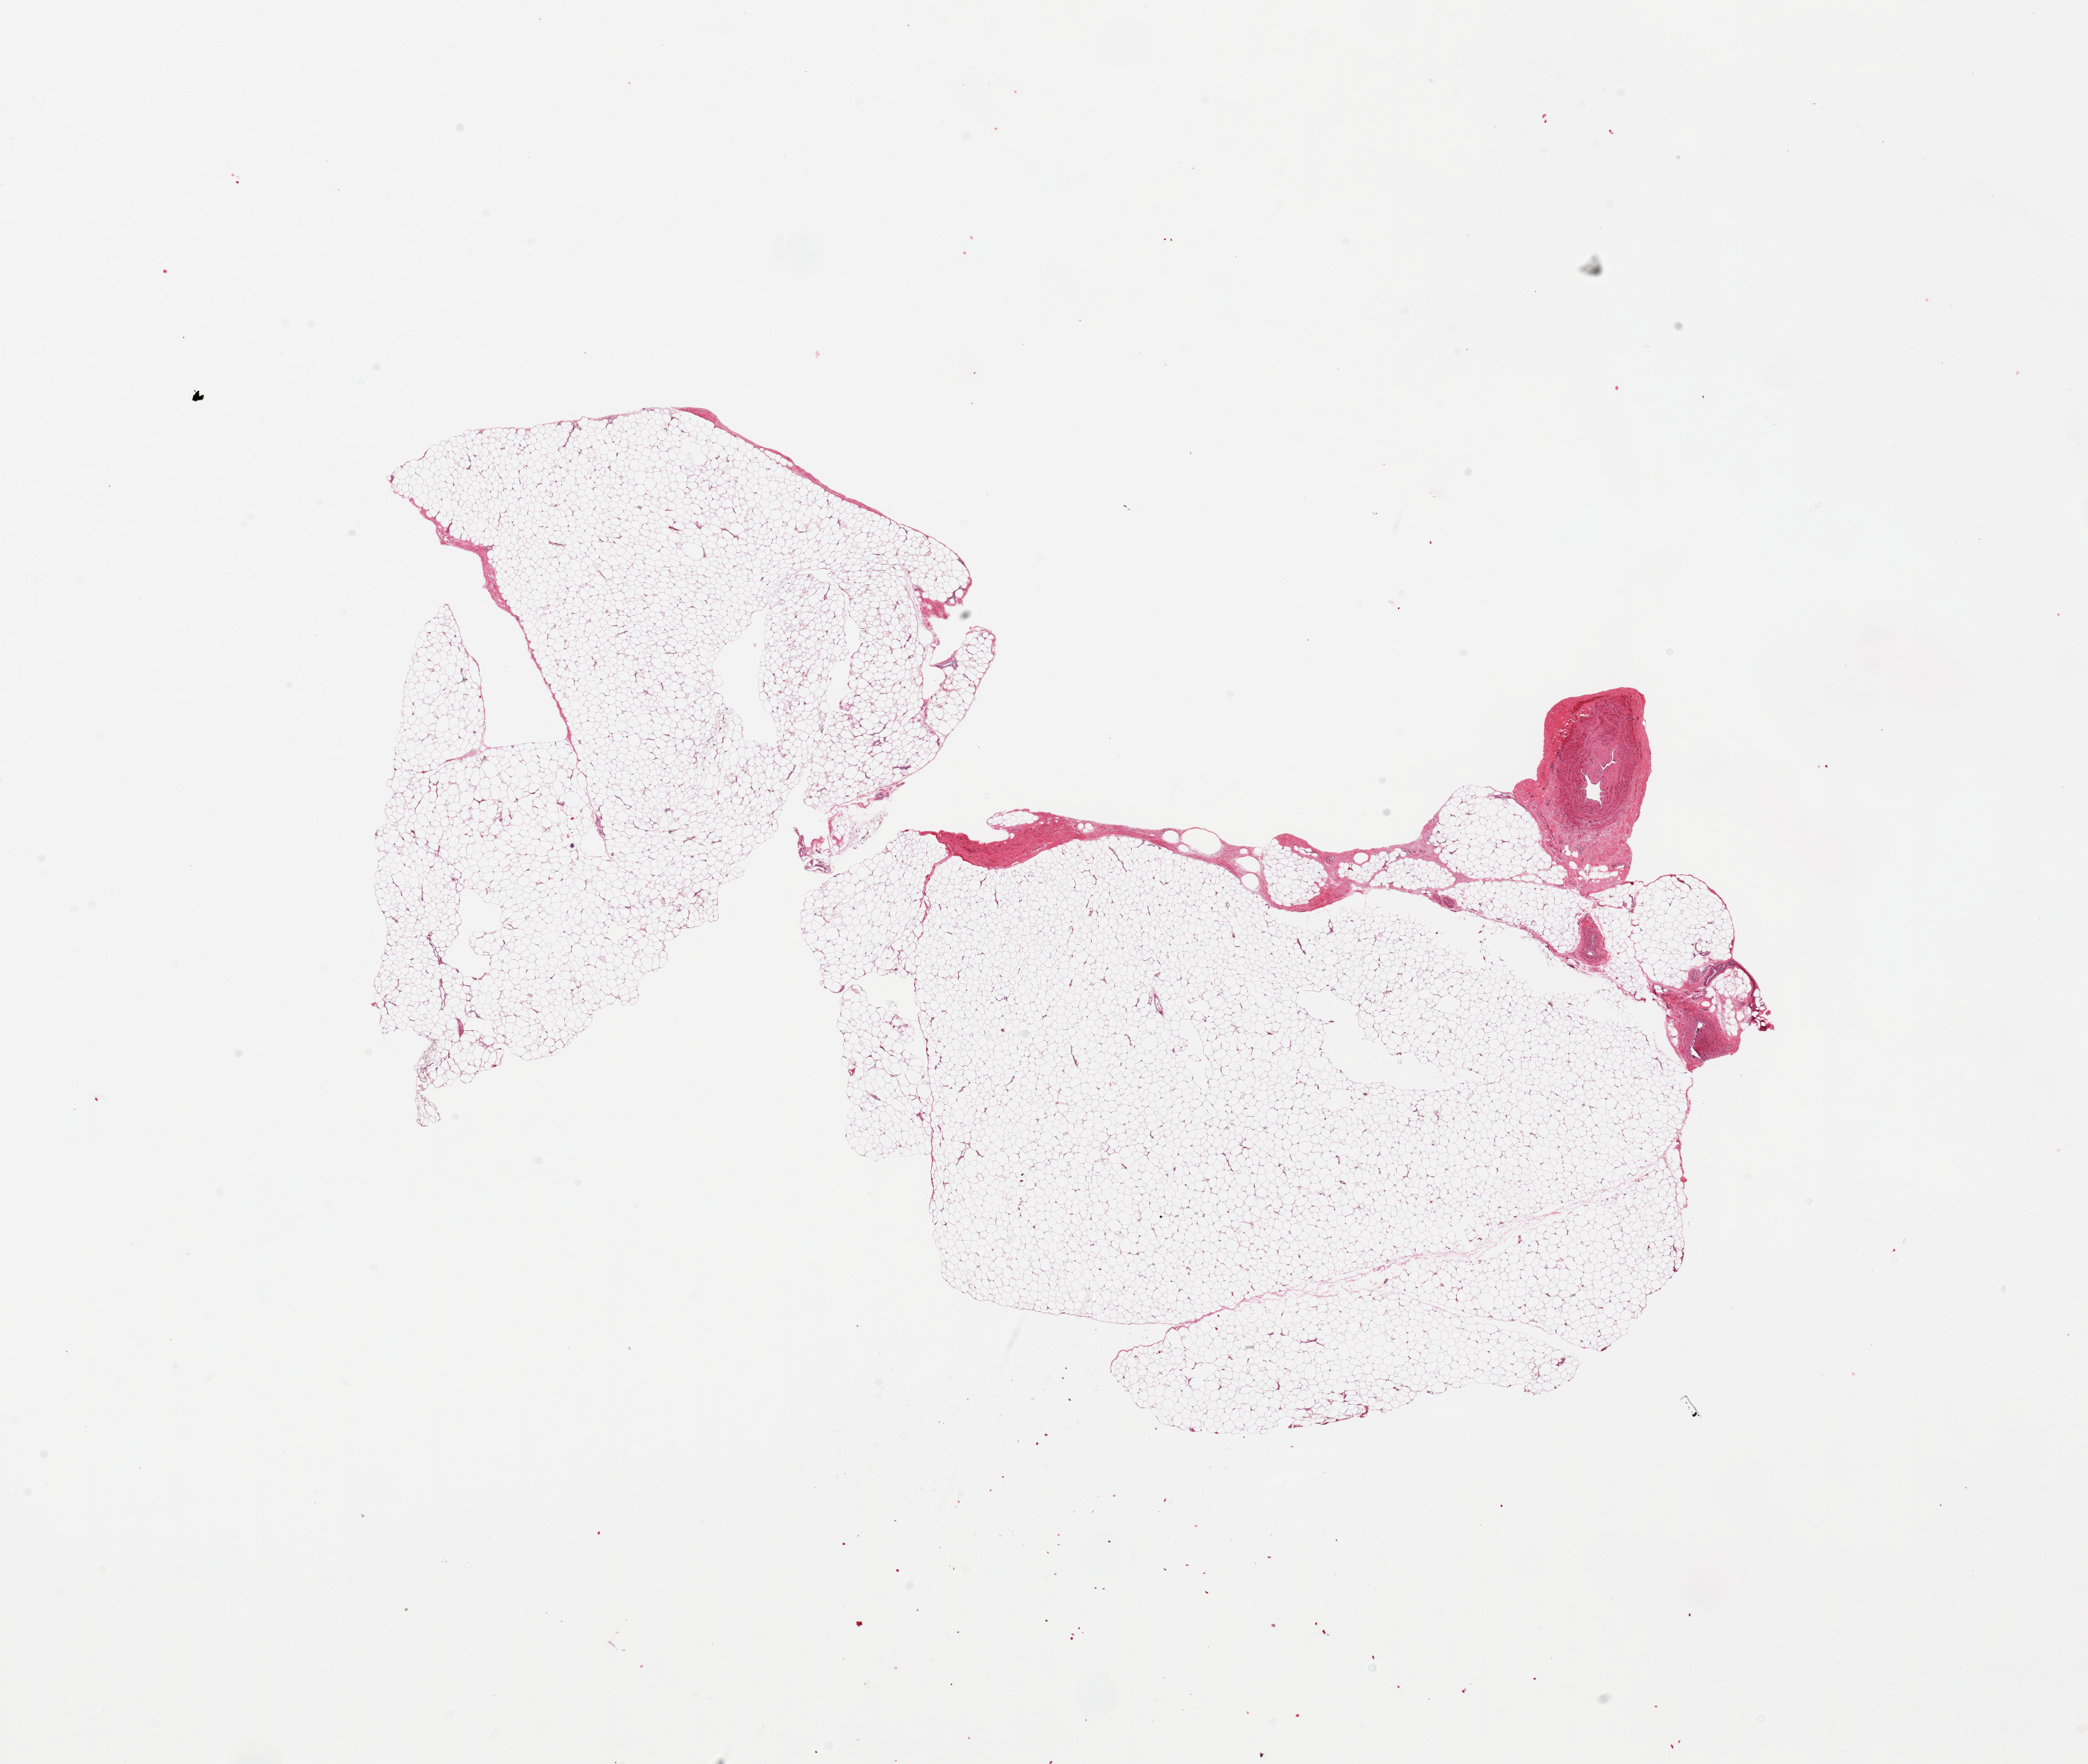
Digitized haematoxylin and eosin-stained section — a low-resolution overview of the entire scanned area, about 23.6 x 20.0 mm; PAXgene-fixed paraffin-embedded (PFPE) section; target tissue: adipose tissue; donor tissue sample.
* pathologist's review note for this sample: 2 pieces; one piece contains ~5% fibrous tissue and vessels